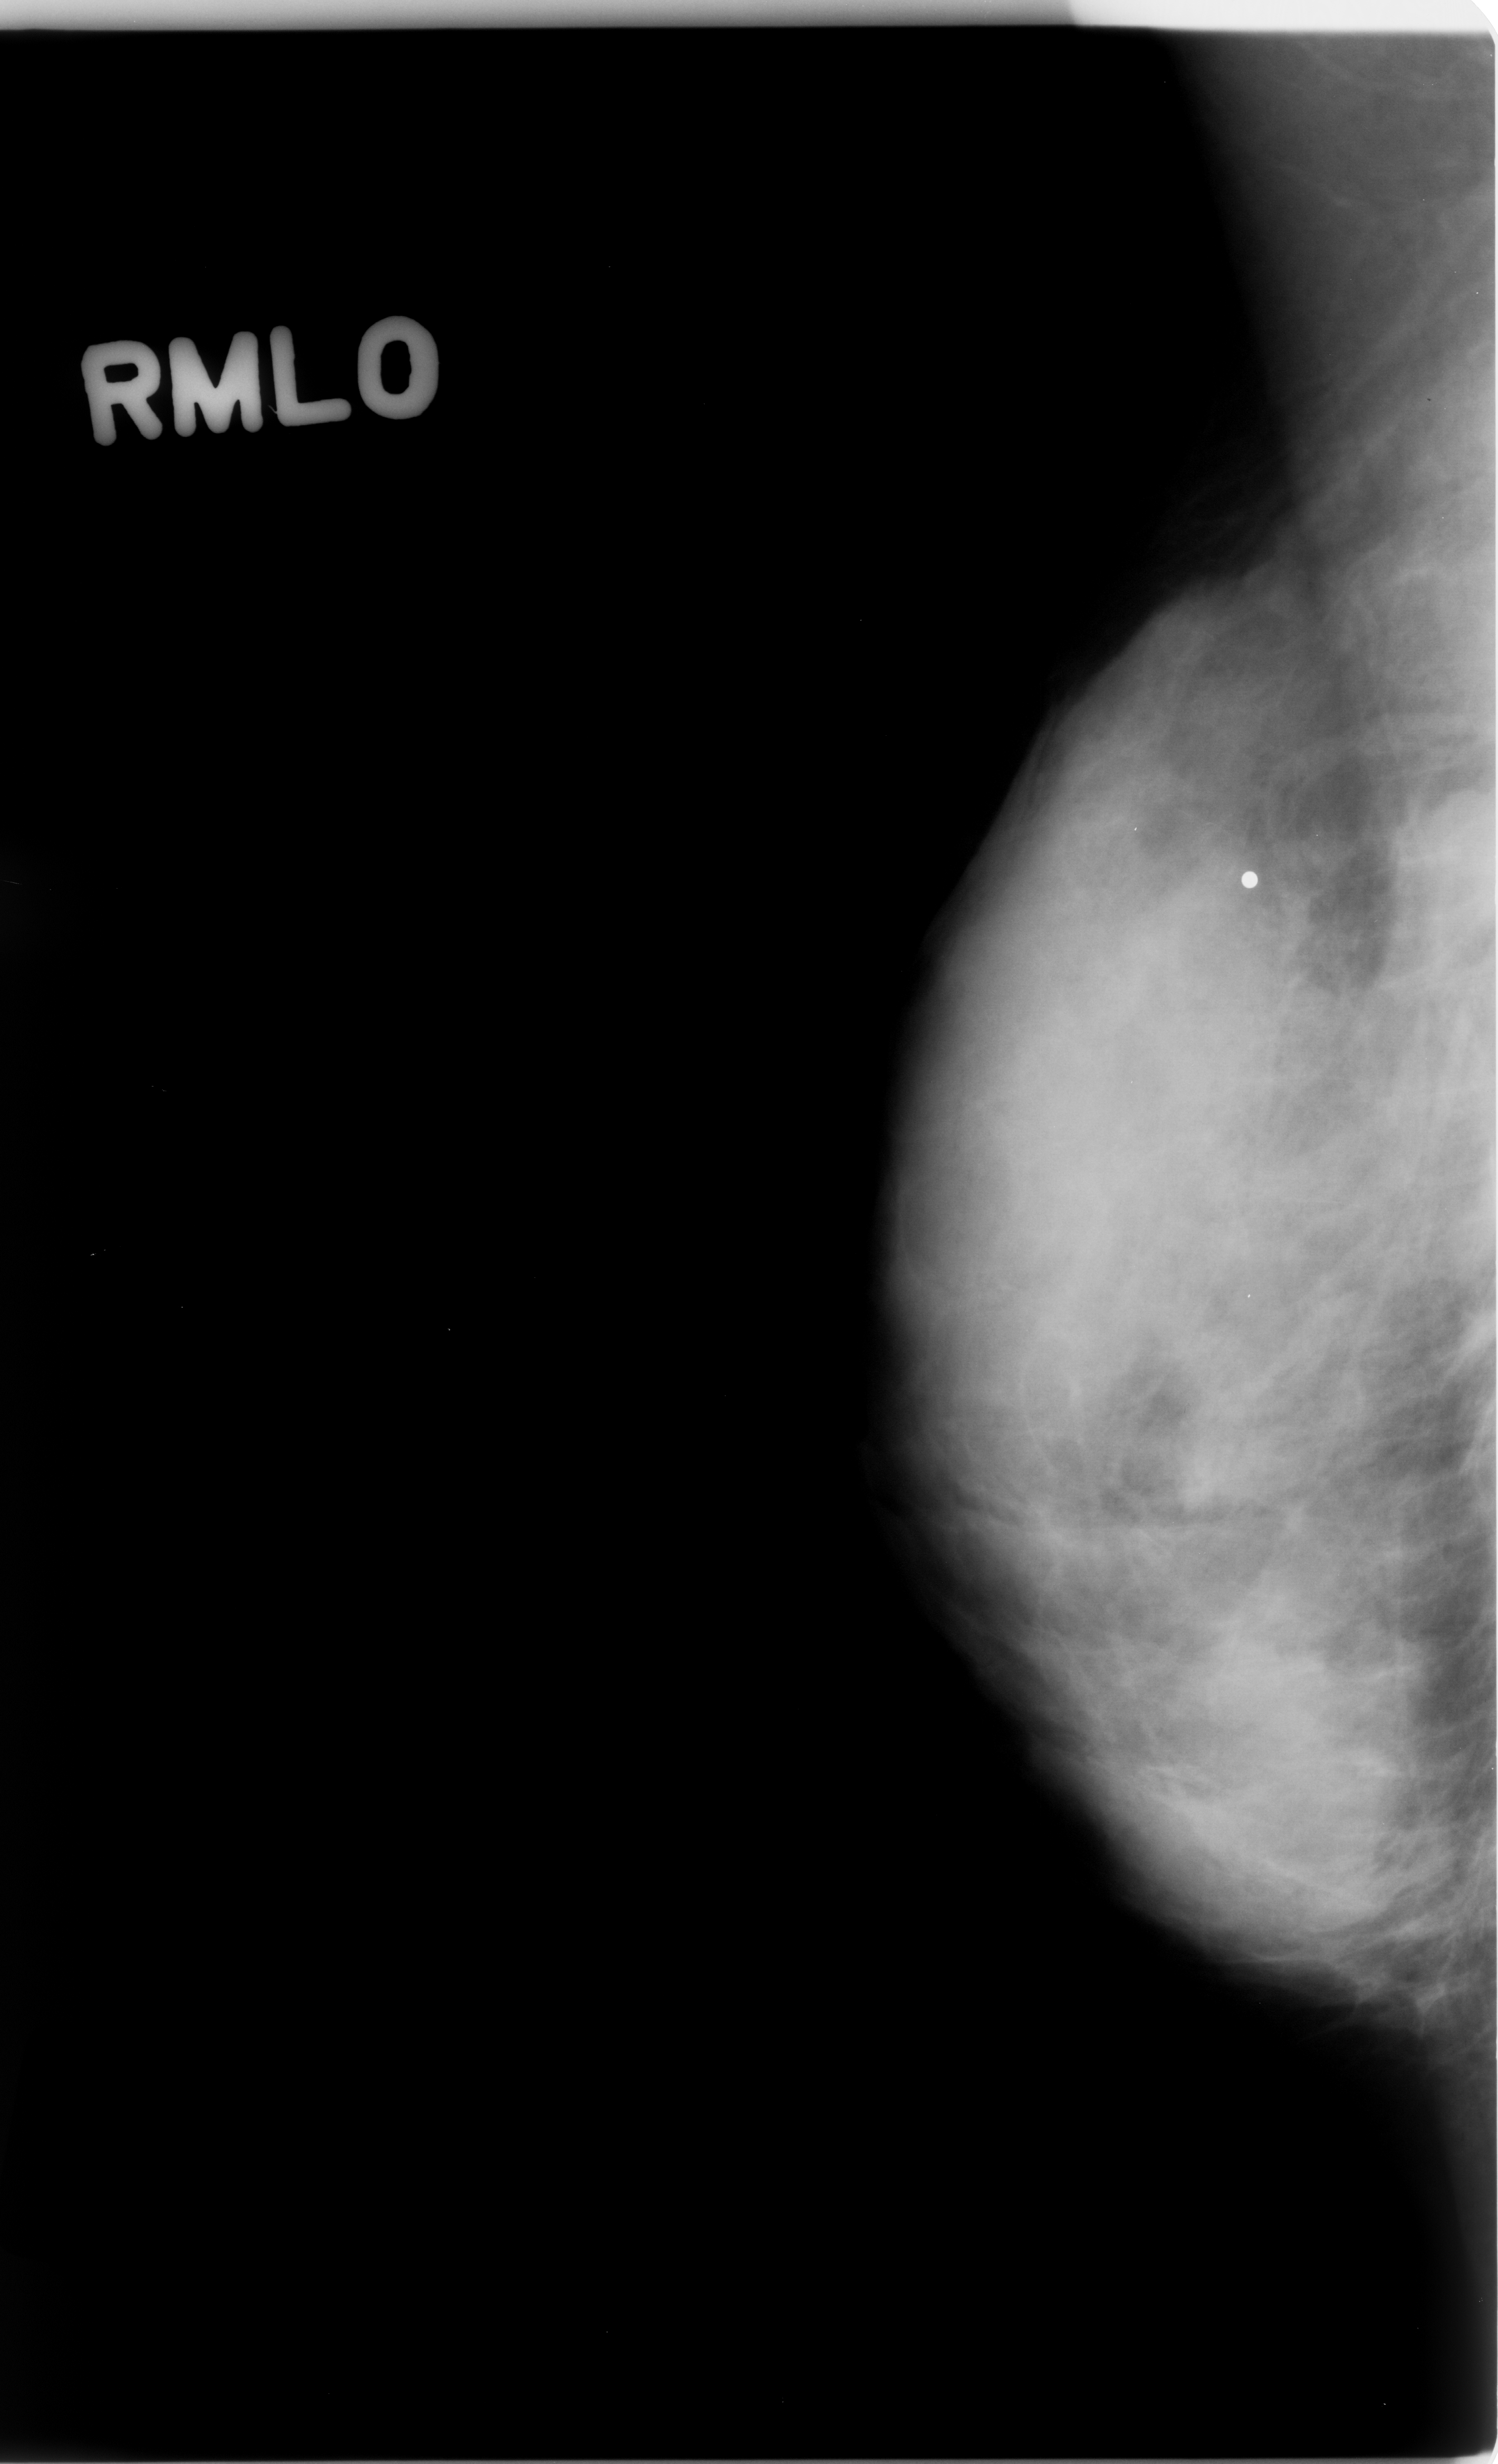
Digitized screen-film mammogram, right breast, MLO view, breast composition: extremely dense (BI-RADS density category 4 of 4).
Marked abnormality: mass, shape oval, margins obscured; BI-RADS assessment category 4; subtlety rating 4 on a 1 (subtle) to 5 (obvious) scale; pathology result (as recorded, not read from the image): benign.